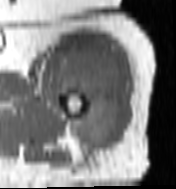
MRI of an extremity soft-tissue mass, one axial slice. Position 83 of 100 along the scan axis. MR volume resampled by the dataset authors to the PET/CT grid (not the native acquisition matrix). 3.27 mm slice thickness. 176 × 189 image matrix, field of view 172 × 185 mm. Female patient. Case-level facts recorded for this patient, not image findings: histological type: undifferentiated – high grade; grade: high; site of the primary tumour: left thigh.
Annotated regions visible in this slice (expert contour drawn on MRI and transferred to this co-registered scan by the dataset authors):
- gross tumour volume including surrounding oedema: box from (x=57, y=50) to (x=120, y=151) px
- gross tumour volume (mass): (x=59, y=52)–(x=120, y=149)